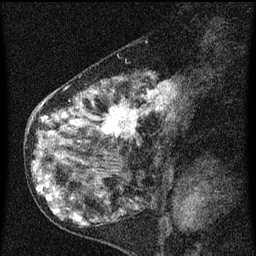
Breast MRI (dynamic contrast-enhanced), one sagittal slice. Position 29 of 60 along the scan axis. Dynamic contrast-enhanced series, image 2 of 3 at this slice position (ordered by acquisition). 1.5 T. TE 4.2 ms, TR 8 ms. 2 mm slice thickness. 256 × 256 image matrix, field of view 180 × 180 mm. Patient: female, 55 years.
Annotated regions visible in this slice (semi-automatically segmented with operator editing):
- analysis volume of interest (the breast-tissue region the enhancement analysis was run in; not a lesion): bounding box <42,72,184,155> (left, top, right, bottom; pixels)
- tumour enhancement mask (voxels above the 70 % enhancement threshold inside the analysis volume of interest): <42,82,176,139>